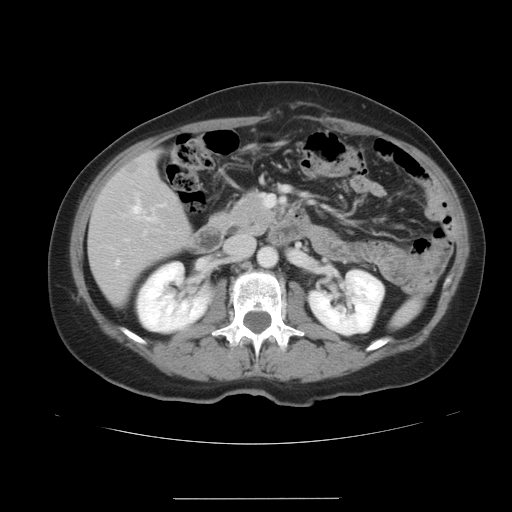
Contrast-enhanced abdominal CT, one axial slice; position 16 of 41 along the scan axis; intravenous contrast given; soft-tissue window (W 400 / L 40 HU); 5 mm slice thickness; 512 × 512 image matrix. Female patient, age 63 years. Case-level facts recorded for this patient, not image findings: diagnosis: colorectal cancer liver metastases, imaged before liver resection; multiple liver metastases: yes; largest metastasis: 1.5 cm; chemotherapy before resection: no.
Outlined on this slice (manually delineated by an expert):
- hepatic veins: bounding box (x1, y1, x2, y2) in pixels: (117, 201, 141, 263)
- liver: (90, 154, 192, 303)
- planned liver remnant (the part of the liver to remain after resection): (90, 177, 192, 303)
- portal vein (with intrahepatic branches): (135, 216, 150, 220)
- liver metastasis: (126, 162, 138, 174)